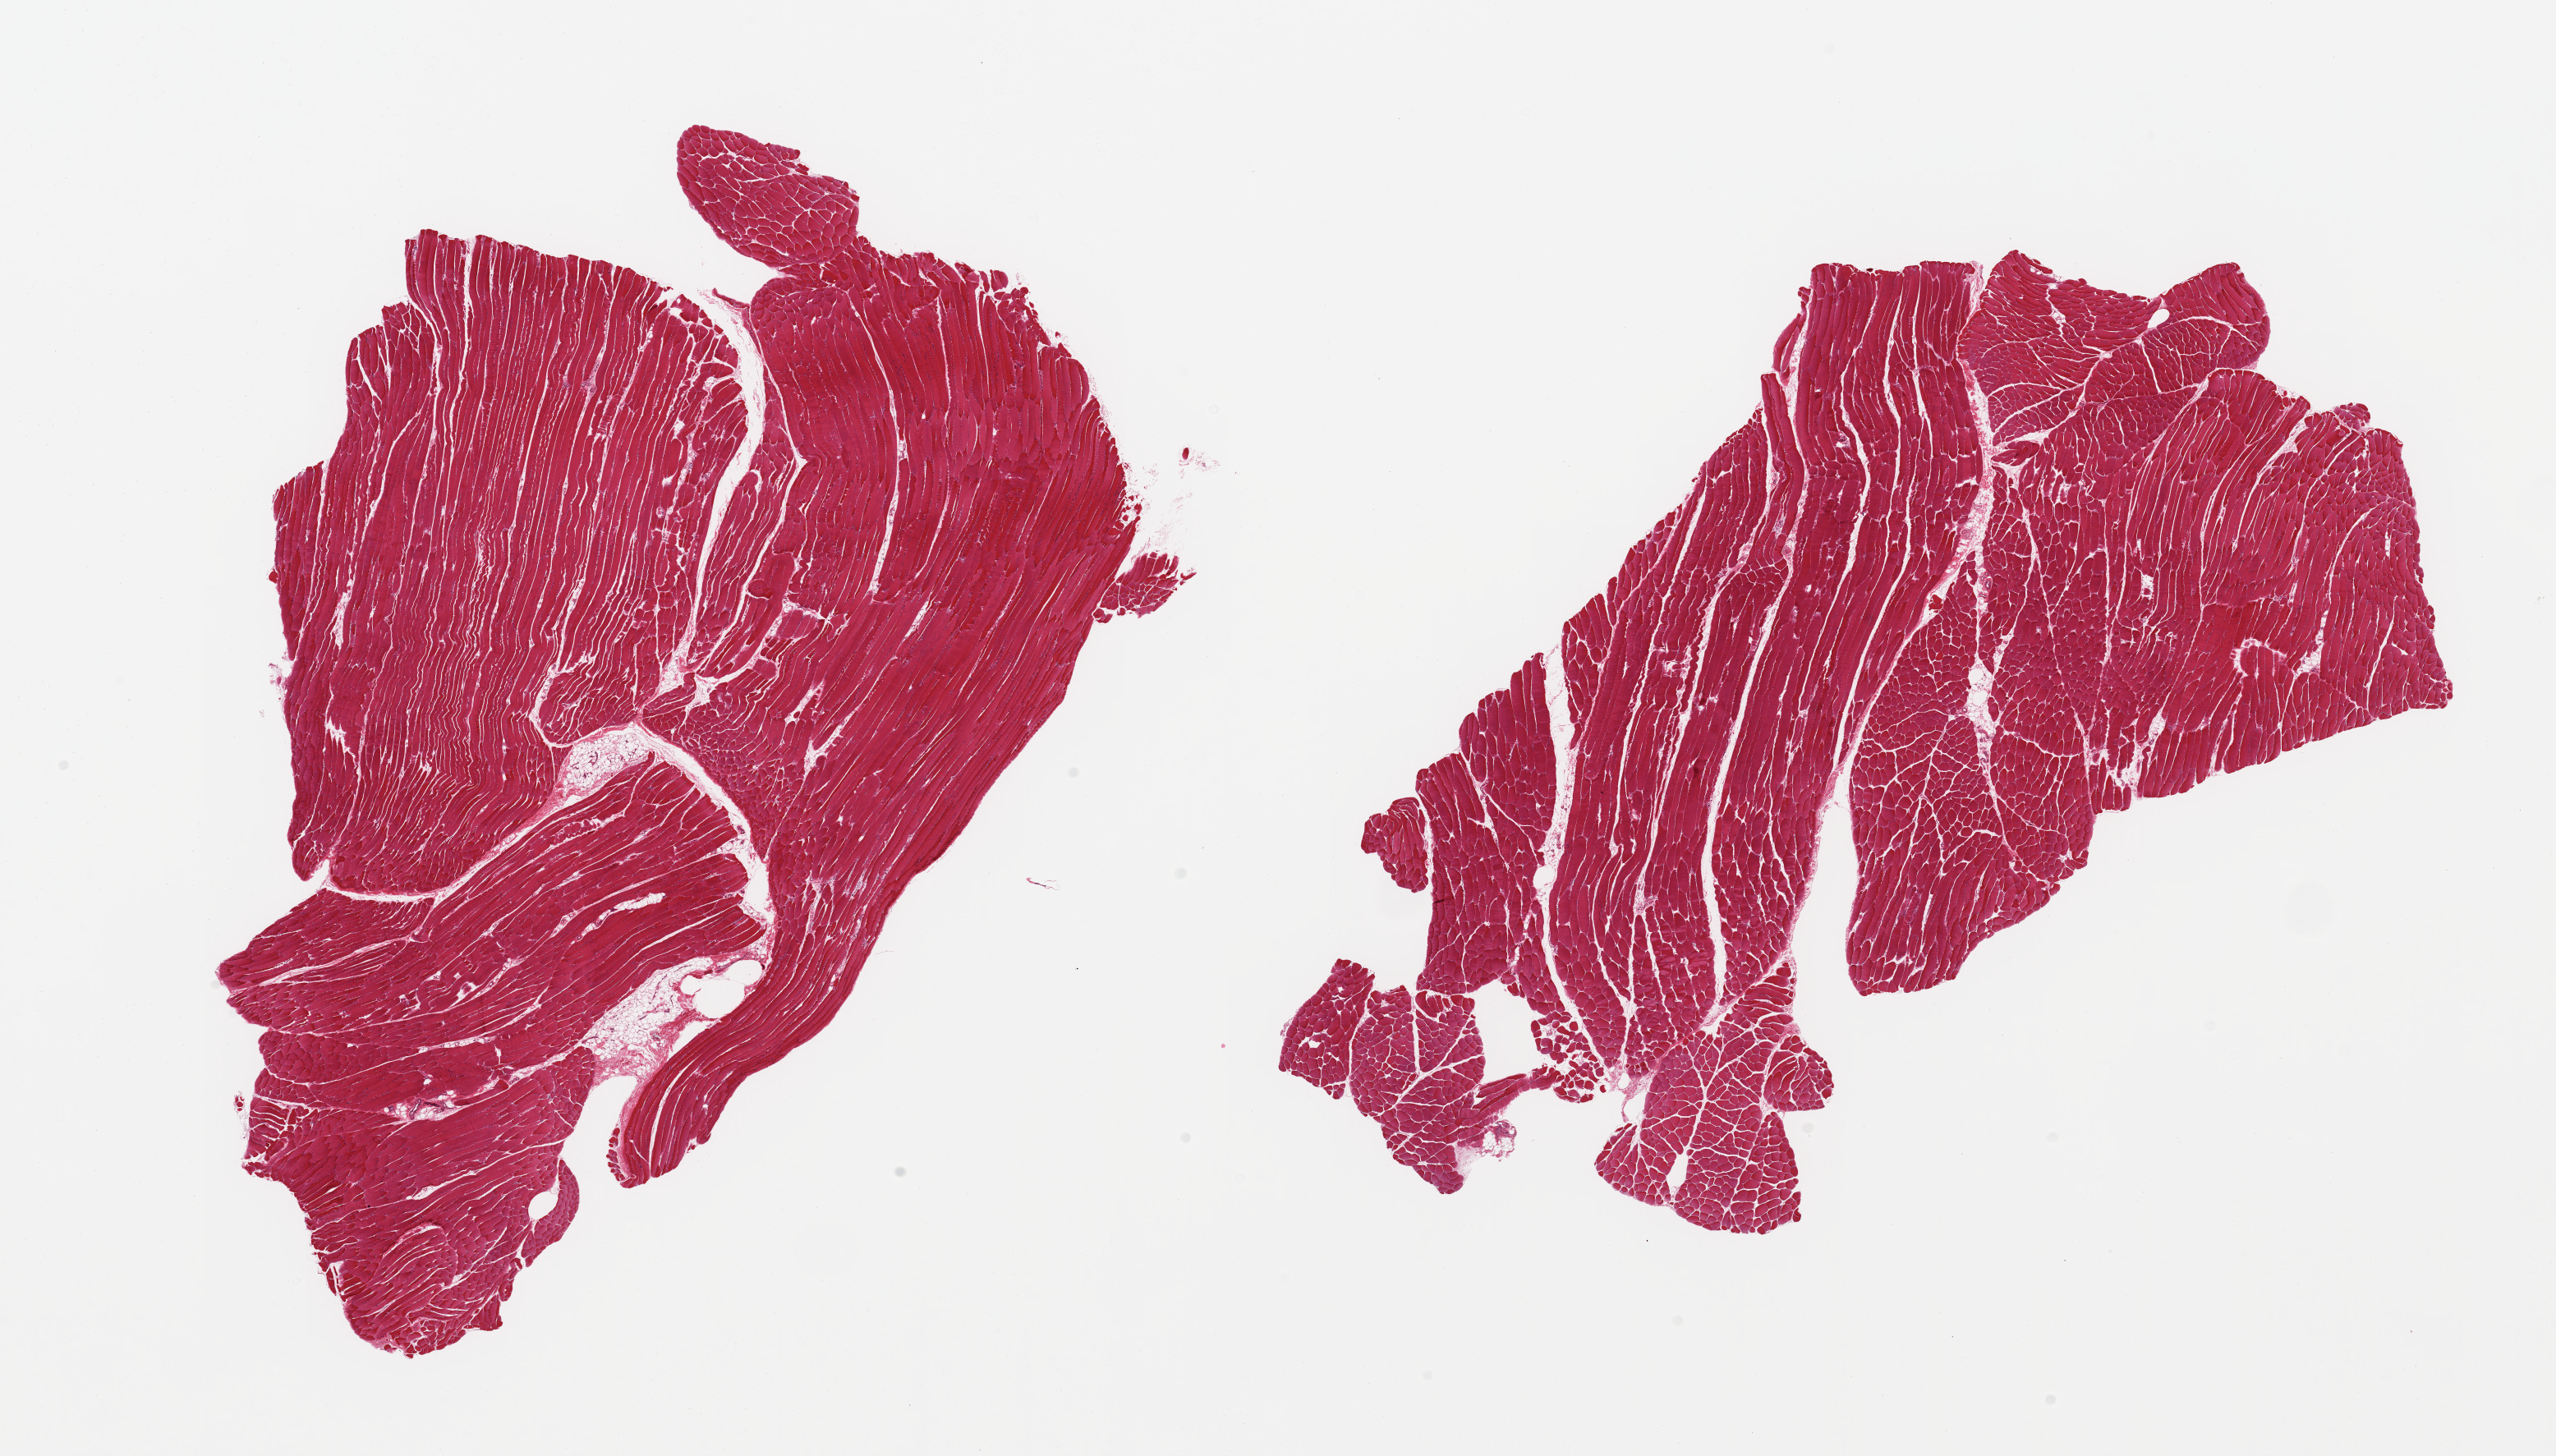
Haematoxylin and eosin whole-slide image, whole scanned area (about 24.6 x 14.0 mm, acquisition: 20x scan) shown as a low-resolution overview; PAXgene-fixed paraffin-embedded (PFPE) section; target tissue: skeletal muscle; tissue donor sample. Donor sex: female.
Reviewer comment on this tissue sample: 2 pieces.